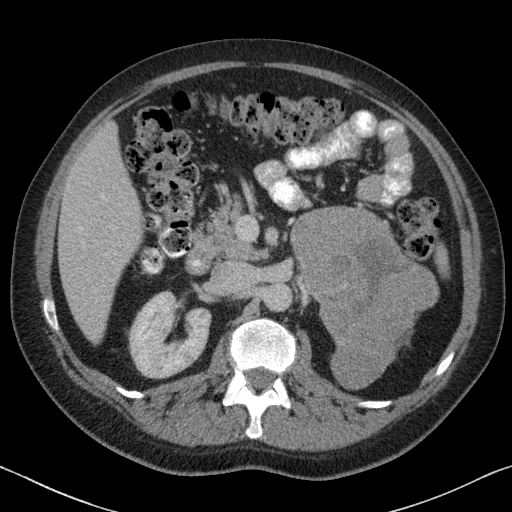
Contrast-enhanced abdominal CT, one axial slice. Position 41 of 88 along the scan axis. 120 kVp. Soft-tissue window (W 400 / L 40 HU). 3 mm slice thickness. 512 × 512 image matrix, field of view 366 × 366 mm. Patient: male, 51 years. Case-level facts recorded for this patient, not image findings: diagnosis: adrenocortical carcinoma; tumour side: left adrenal; tumour size at pathology: 16.5 cm; Ki-67 index: 30 %; stage (as recorded): 2.
Structures marked on this image (semi-automatically segmented with operator editing):
- mass: bounding box (x1, y1, x2, y2) in pixels: (291, 207, 438, 389)